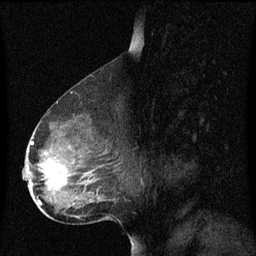
Breast MRI (dynamic contrast-enhanced), one sagittal slice. Slice 39 of 60 in the series (ordered by position). Dynamic contrast-enhanced series, image 2 of 3 at this slice position (ordered by acquisition). 1.5 T. TE 4.2 ms, TR 8.4 ms. 256 × 256 image matrix. Patient: female, 49 years. Case-level facts recorded for this patient, not image findings: setting: breast cancer imaged before/during neoadjuvant chemotherapy; receptor status: HR-positive, HER2-negative.
Outlined on this slice (semi-automatic segmentation, software-assisted and operator-edited):
- analysis volume of interest (the breast-tissue region the enhancement analysis was run in; not a lesion): bounding box (x1, y1, x2, y2) in pixels: (24, 126, 108, 201)
- tumour enhancement mask (voxels above the 70 % enhancement threshold inside the analysis volume of interest): (30, 142, 69, 189)